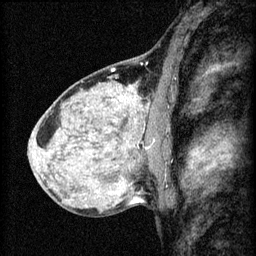
Breast MRI (dynamic contrast-enhanced), one sagittal slice. Slice 37 of 60 in the series (ordered by position). 3 images stored at this slice position (order not interpretable as contrast timing). 1.5 T. TE 4.2 ms, TR 8.2 ms. 2 mm slice thickness. 256 × 256 image matrix, field of view 180 × 180 mm. Patient: female, 40 years.
Structures marked on this image (semi-automatically segmented with operator editing):
- analysis volume of interest (the breast-tissue region the enhancement analysis was run in; not a lesion): box from (x=108, y=108) to (x=167, y=159) px
- tumour enhancement mask (voxels above the 70 % enhancement threshold inside the analysis volume of interest): (x=148, y=140)–(x=155, y=149)